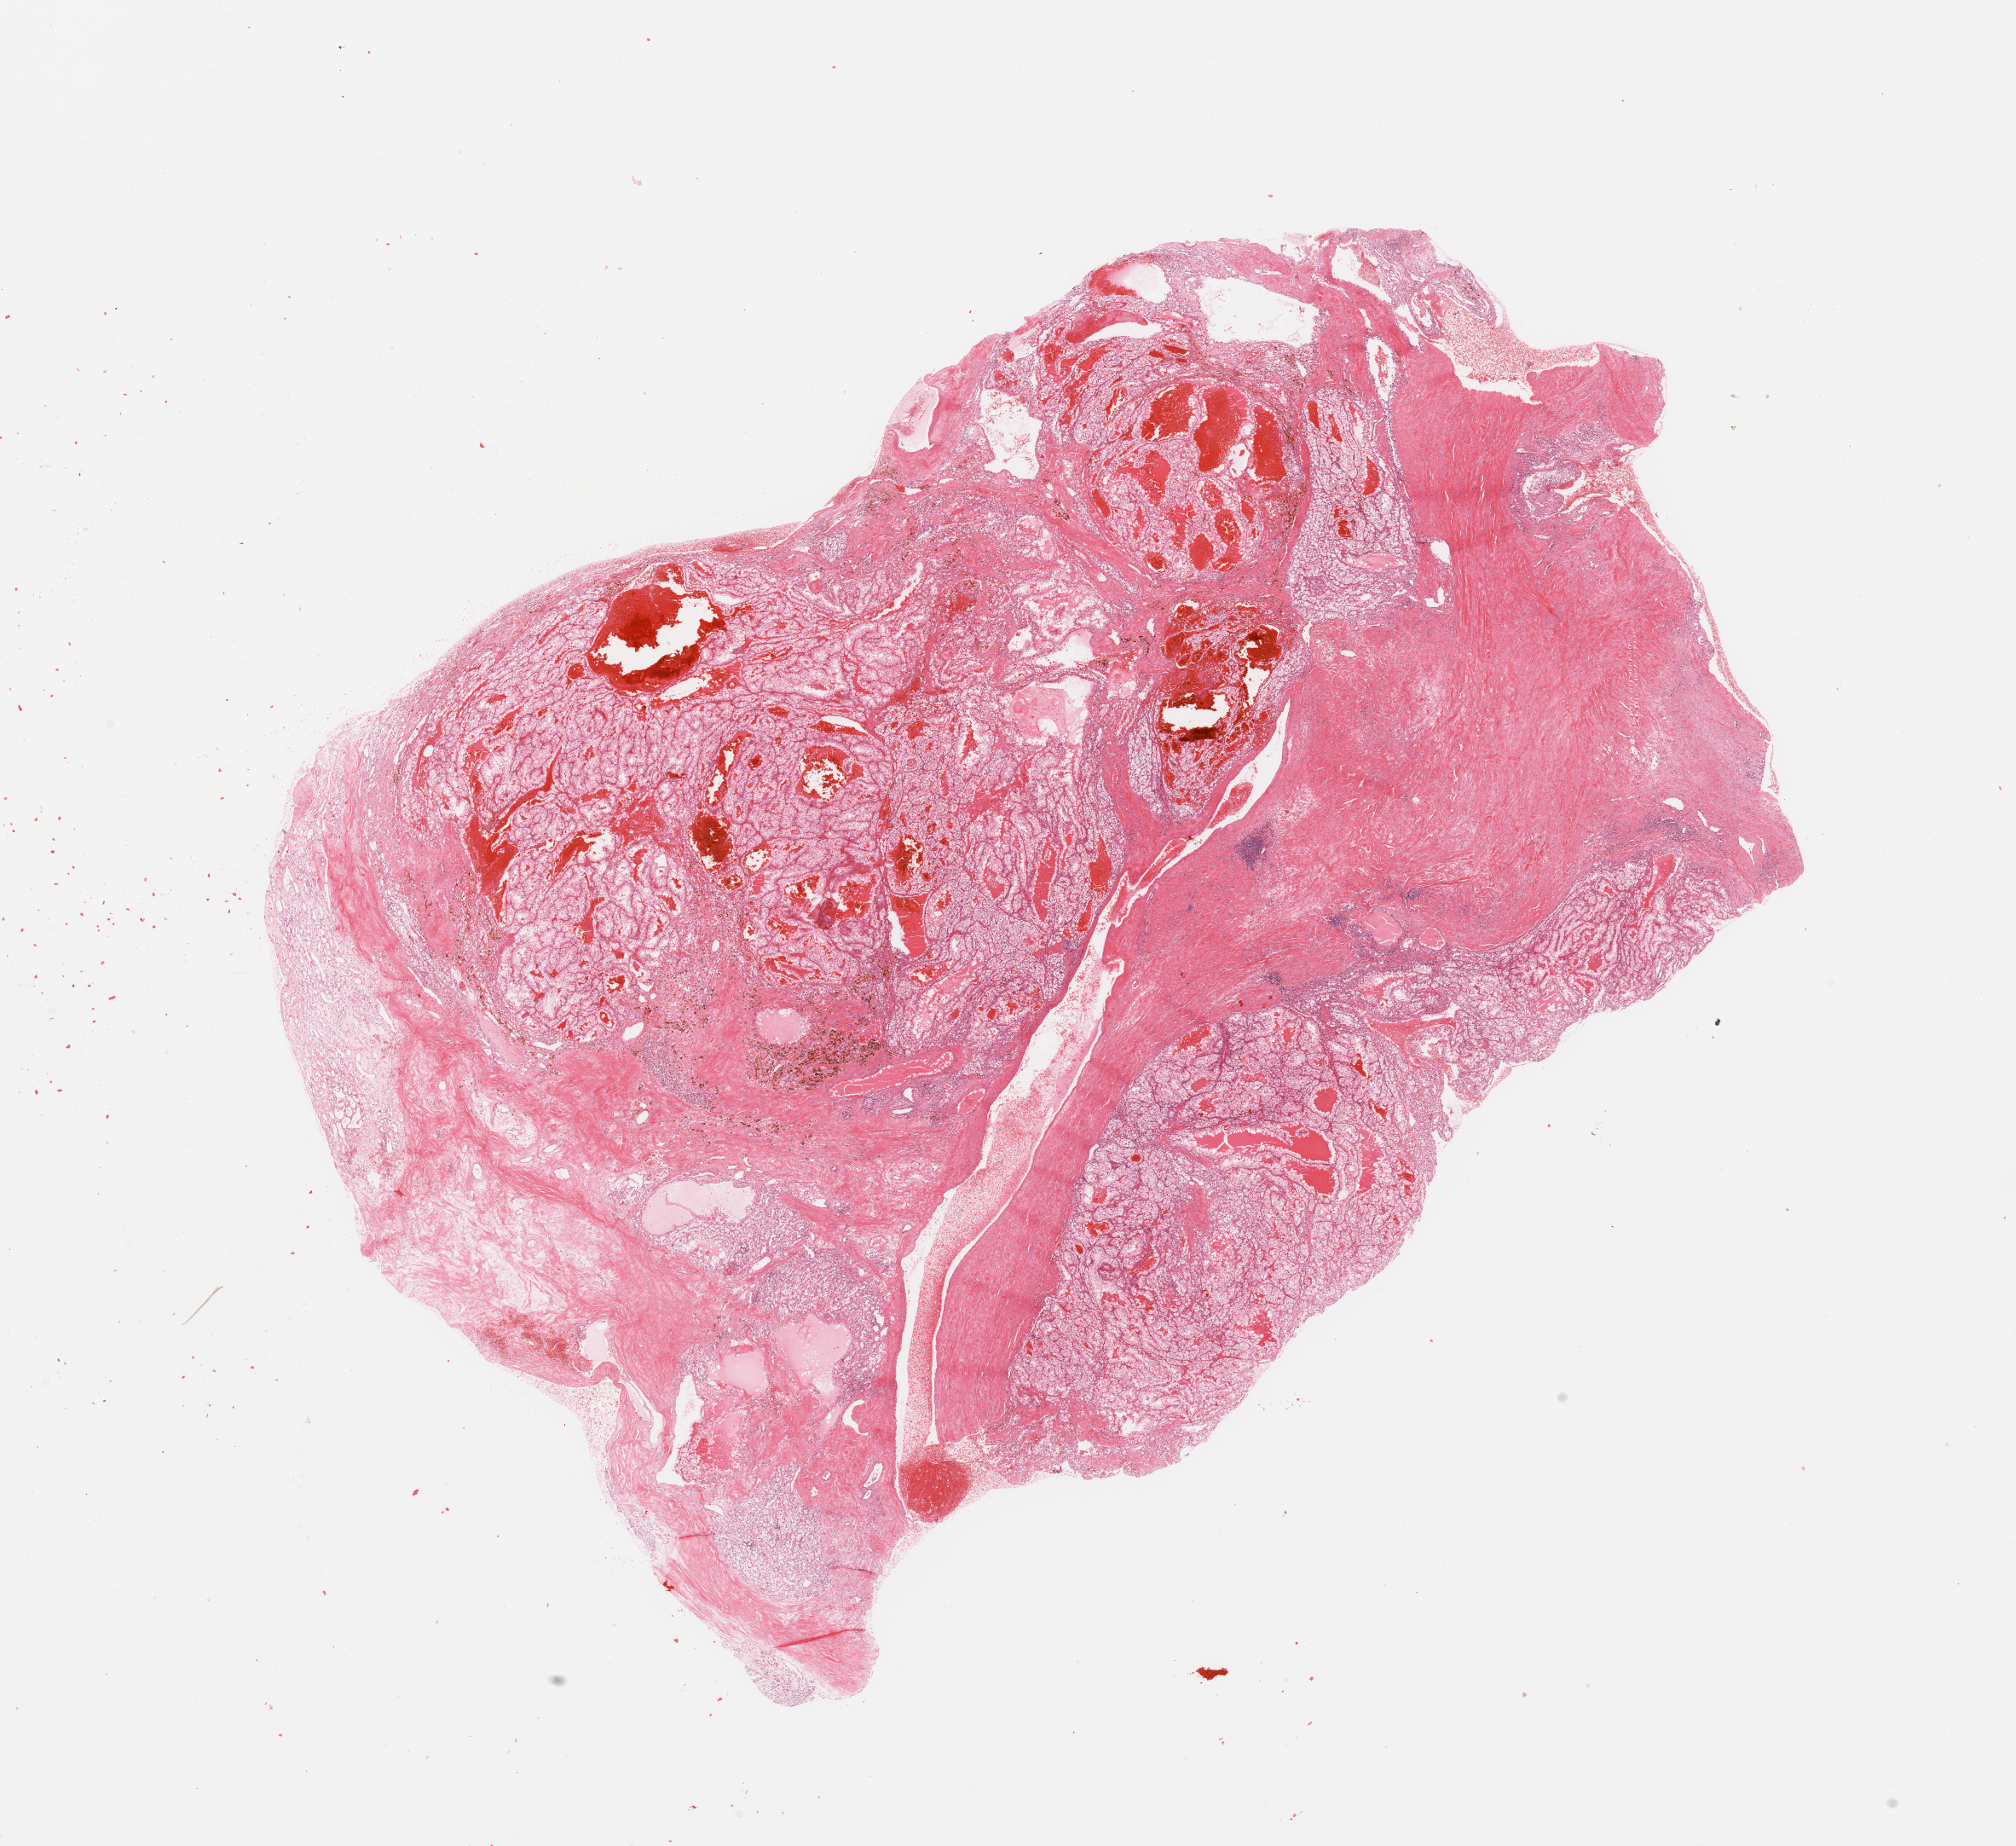
Digitized H&E-stained tissue section (whole slide), shown as a low-resolution overview of the whole scanned area (about 18.7 x 17.1 mm); tumour tissue sample, sampled site: kidney. Patient: female, age 55 years. Histologic grade: G3 (poorly differentiated). Composition of this section per pathologist review: tumour nuclei 90%, necrosis 5%.
AJCC pathologic stage: IV. Histologic diagnosis: Renal cell carcinoma, NOS.